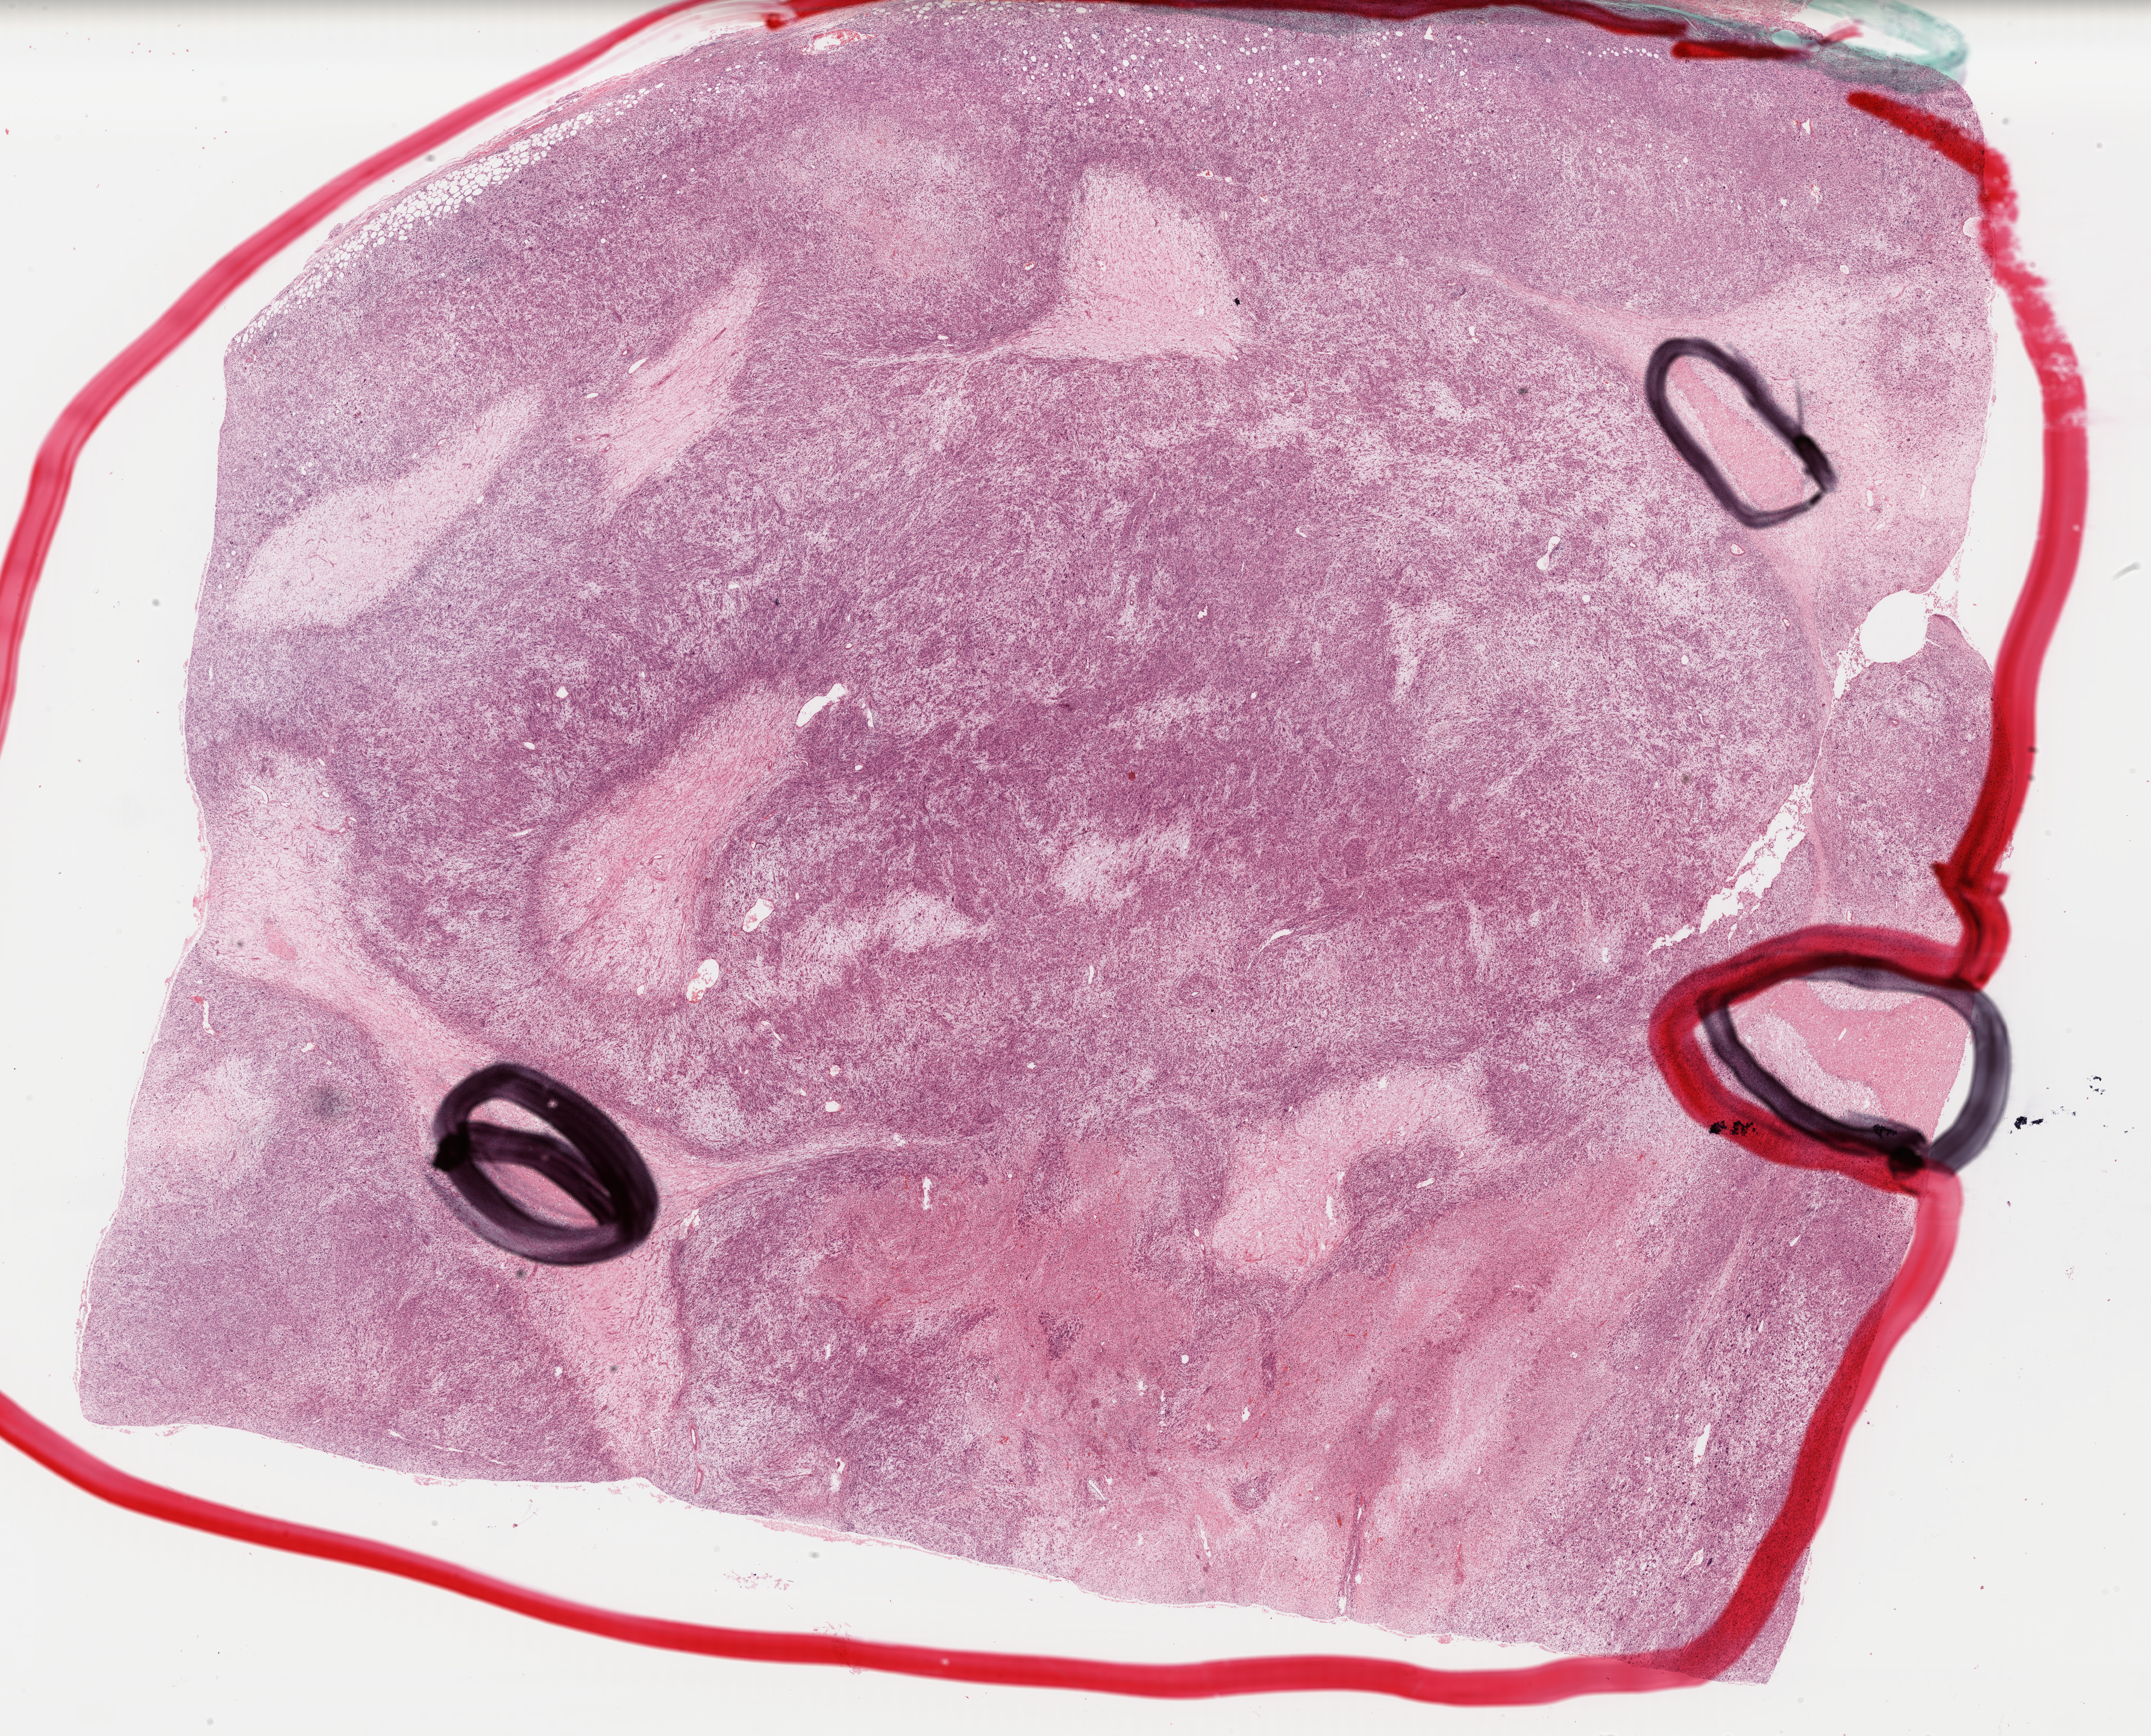
Digitized H&E tissue section (whole slide) — whole scanned area (about 28.2 x 22.7 mm, acquisition: 40x scan) shown as a low-resolution overview. FFPE section. Sample: primary tumour, connective, subcutaneous and other soft tissues. Female patient.
Histologic diagnosis: Pleomorphic liposarcoma (connective, subcutaneous and other soft tissues of lower limb and hip).